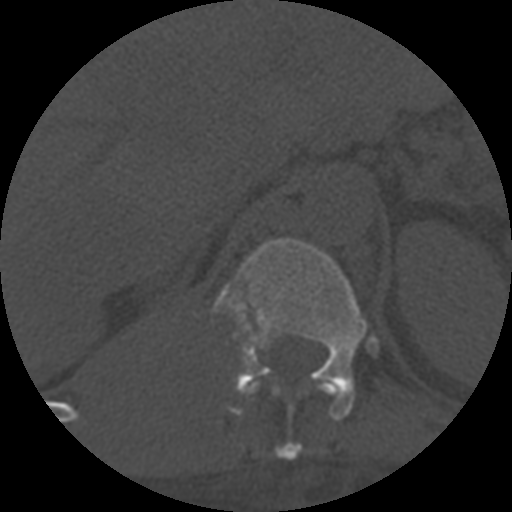
CT including the spine, one axial slice. Slice 321 of 708 in the series (ordered by position). One of 3 acquisitions stored at this slice position. Bone window (W 1800 / L 400 HU). 1.25 mm slice thickness. 512 × 512 image matrix. Patient age 55 years. Case-level facts recorded for this patient, not image findings: primary cancer: colon.
Outlined on this slice (semi-automatic segmentation, software-assisted and operator-edited):
- T11 vertebra: bounding box [x1, y1, x2, y2] px = [243, 380, 342, 460]
- T12 vertebra: [214, 238, 367, 421]